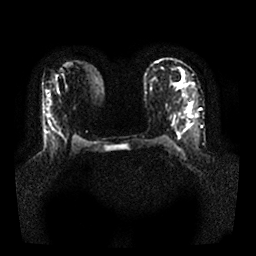
Breast MRI, one axial slice; position 13 of 25 along the scan axis; diffusion-weighted series; image 2 of 4 stored at this slice position (different b-values; order by instance number); 1.5 T; 4 mm slice thickness; 256 × 256 image matrix. Female patient.
Annotated regions visible in this slice (manually delineated by an expert):
- tumour on diffusion-weighted imaging: bounding box <188,104,193,116> (left, top, right, bottom; pixels)